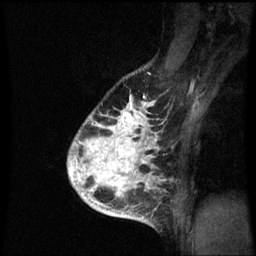
Breast MRI (dynamic contrast-enhanced), one sagittal slice. Position 49 of 60 along the scan axis. Dynamic contrast-enhanced series, image 2 of 3 at this slice position (ordered by acquisition). 1.5 T. TE 4.2 ms, TR 8.9 ms. 256 × 256 image matrix. Female patient, age 35 years. Case-level facts recorded for this patient, not image findings: setting: breast cancer imaged before/during neoadjuvant chemotherapy; receptor status: HR-positive, HER2-negative.
Outlined on this slice (semi-automatic segmentation, software-assisted and operator-edited):
- analysis volume of interest (the breast-tissue region the enhancement analysis was run in; not a lesion): bounding box <69,100,166,215> (left, top, right, bottom; pixels)
- tumour enhancement mask (voxels above the 70 % enhancement threshold inside the analysis volume of interest): <69,102,157,215>